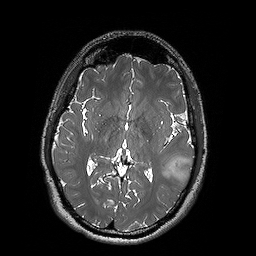
Brain MRI from a brain-tumour surgery series, one axial slice. Slice 90 of 192 in the series (ordered by position). 1 mm slice thickness. 256 × 256 image matrix, field of view 250 × 250 mm. Case-level facts recorded for this patient, not image findings: histopathology: Oligodendroglioma; WHO grade: 2.
Outlined on this slice (manually delineated by an expert):
- tumour: bounding box (x1, y1, x2, y2) in pixels: (159, 155, 193, 180)